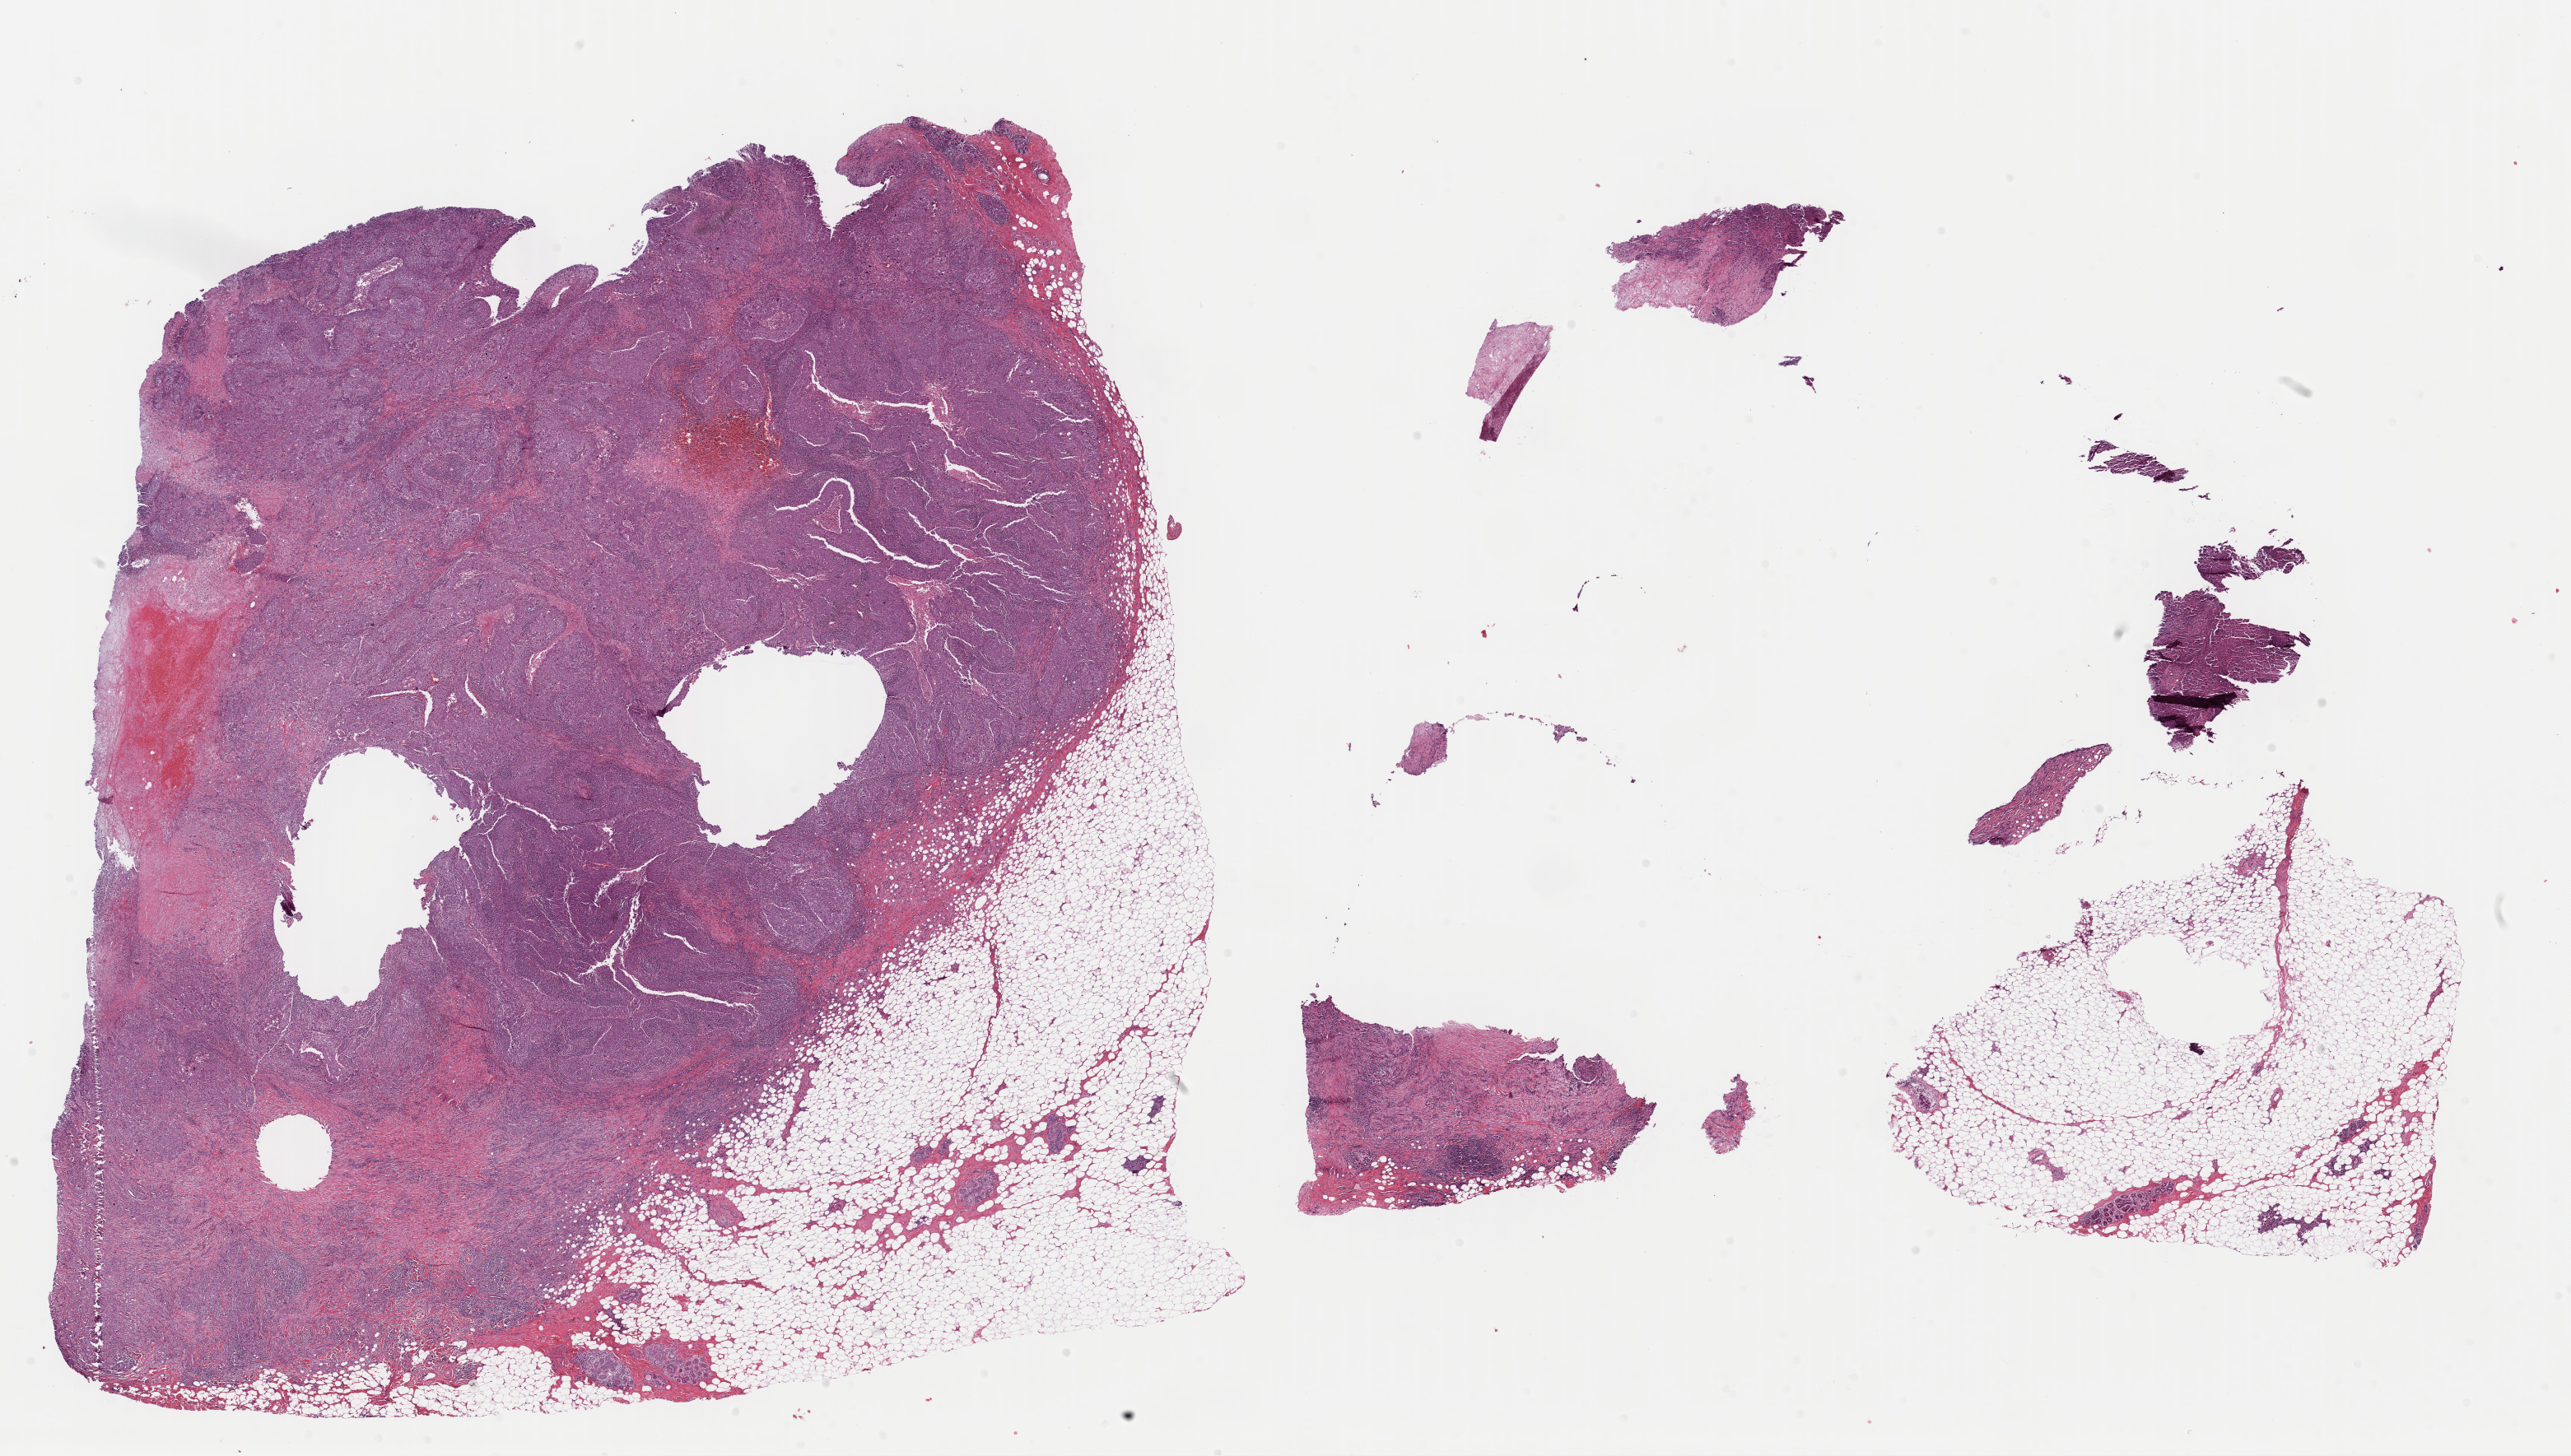
Digitized H&E-stained tissue section (whole slide), a low-resolution overview of the entire scanned area, about 24.7 x 14.0 mm (slide scanned at 40x). Formalin-fixed paraffin-embedded (FFPE) diagnostic section. Sample: primary tumour, breast. Female patient; age at initial diagnosis 49 years.
• lymph nodes positive (case pathology): 0 of 6 examined
• TNM: T2 N0 M0
• diagnosis: Infiltrating duct carcinoma, NOS
• AJCC pathologic stage: IIA
• laterality: right